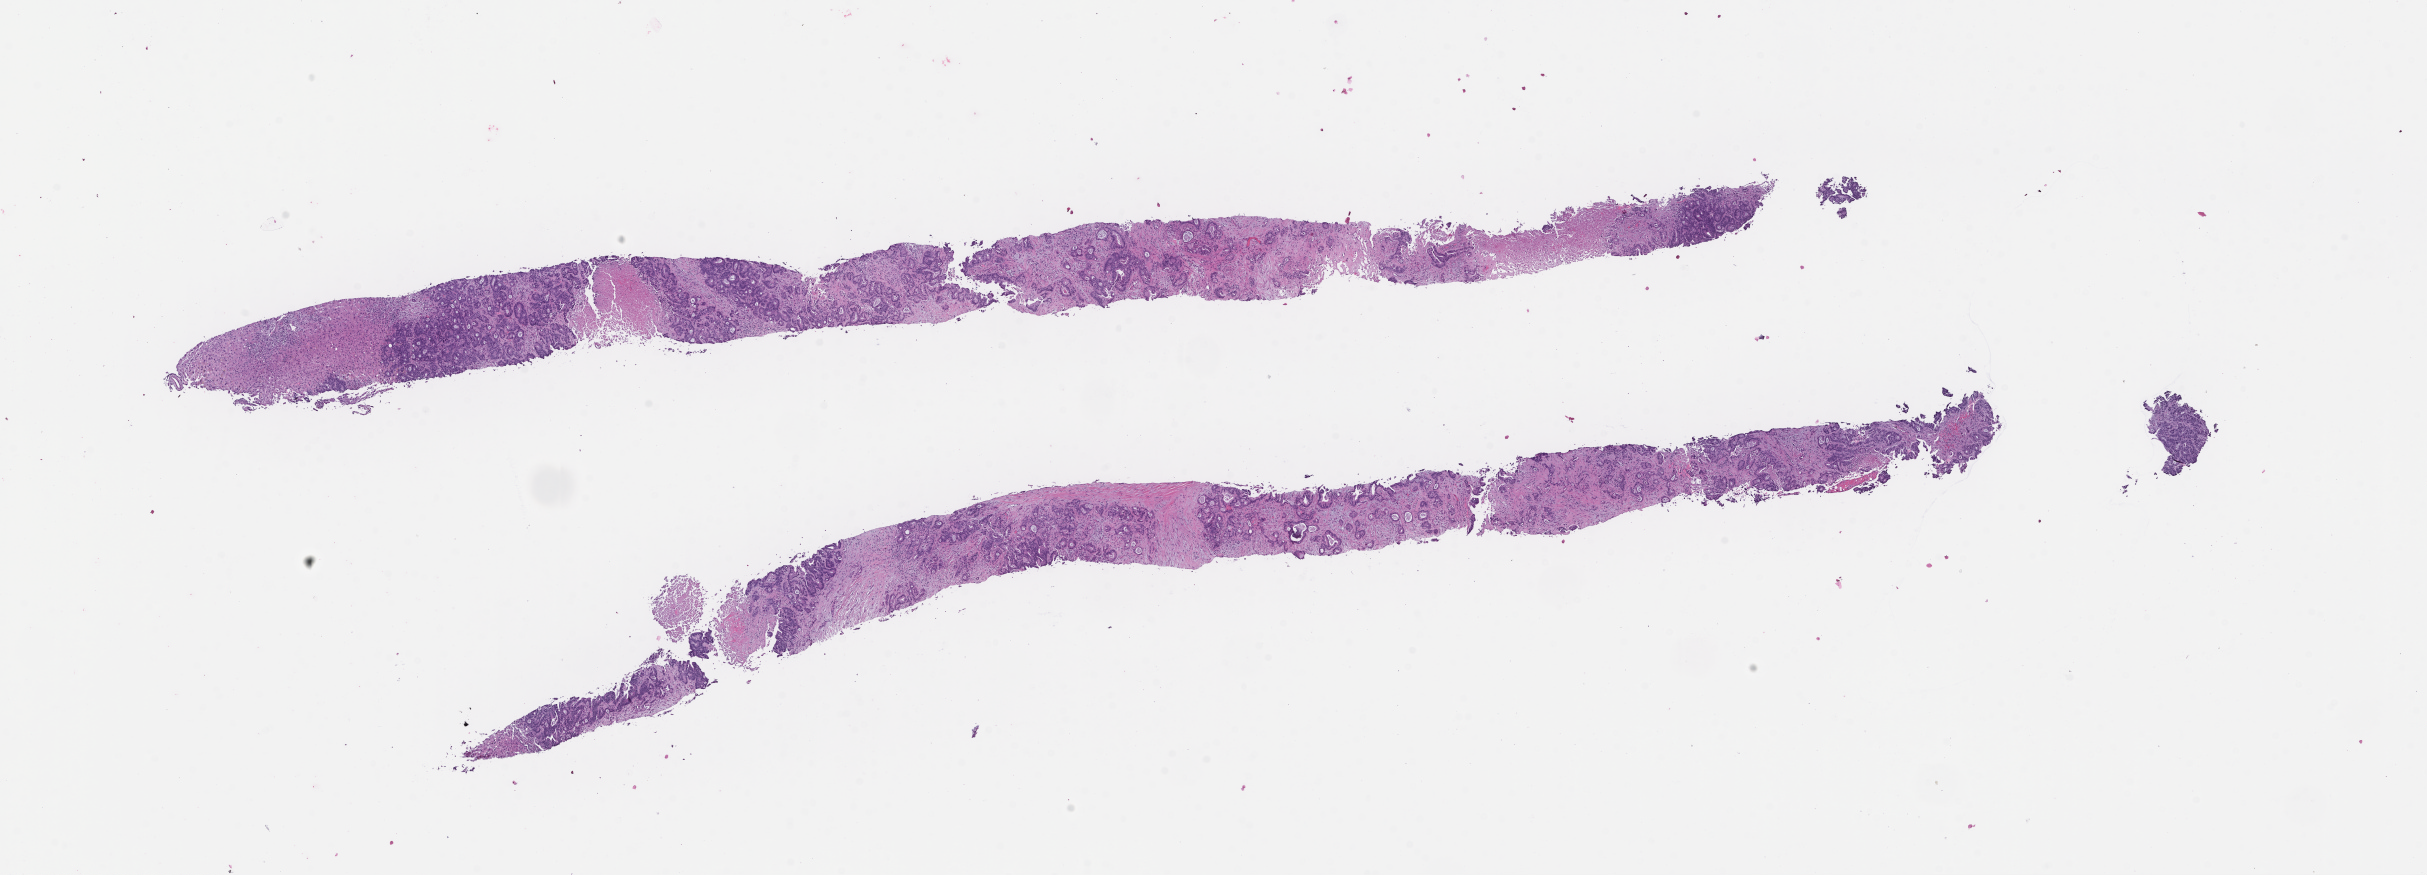
Digitized haematoxylin and eosin-stained section — low-resolution overview of the scanned area, about 19.6 x 7.1 mm; formalin-fixed, paraffin-embedded (FFPE) tissue; specimen time point: archival tissue. Patient: male.
This section: metastasis (sampled organ not recorded). Primary diagnosis of the patient: Colorectal Carcinoma.